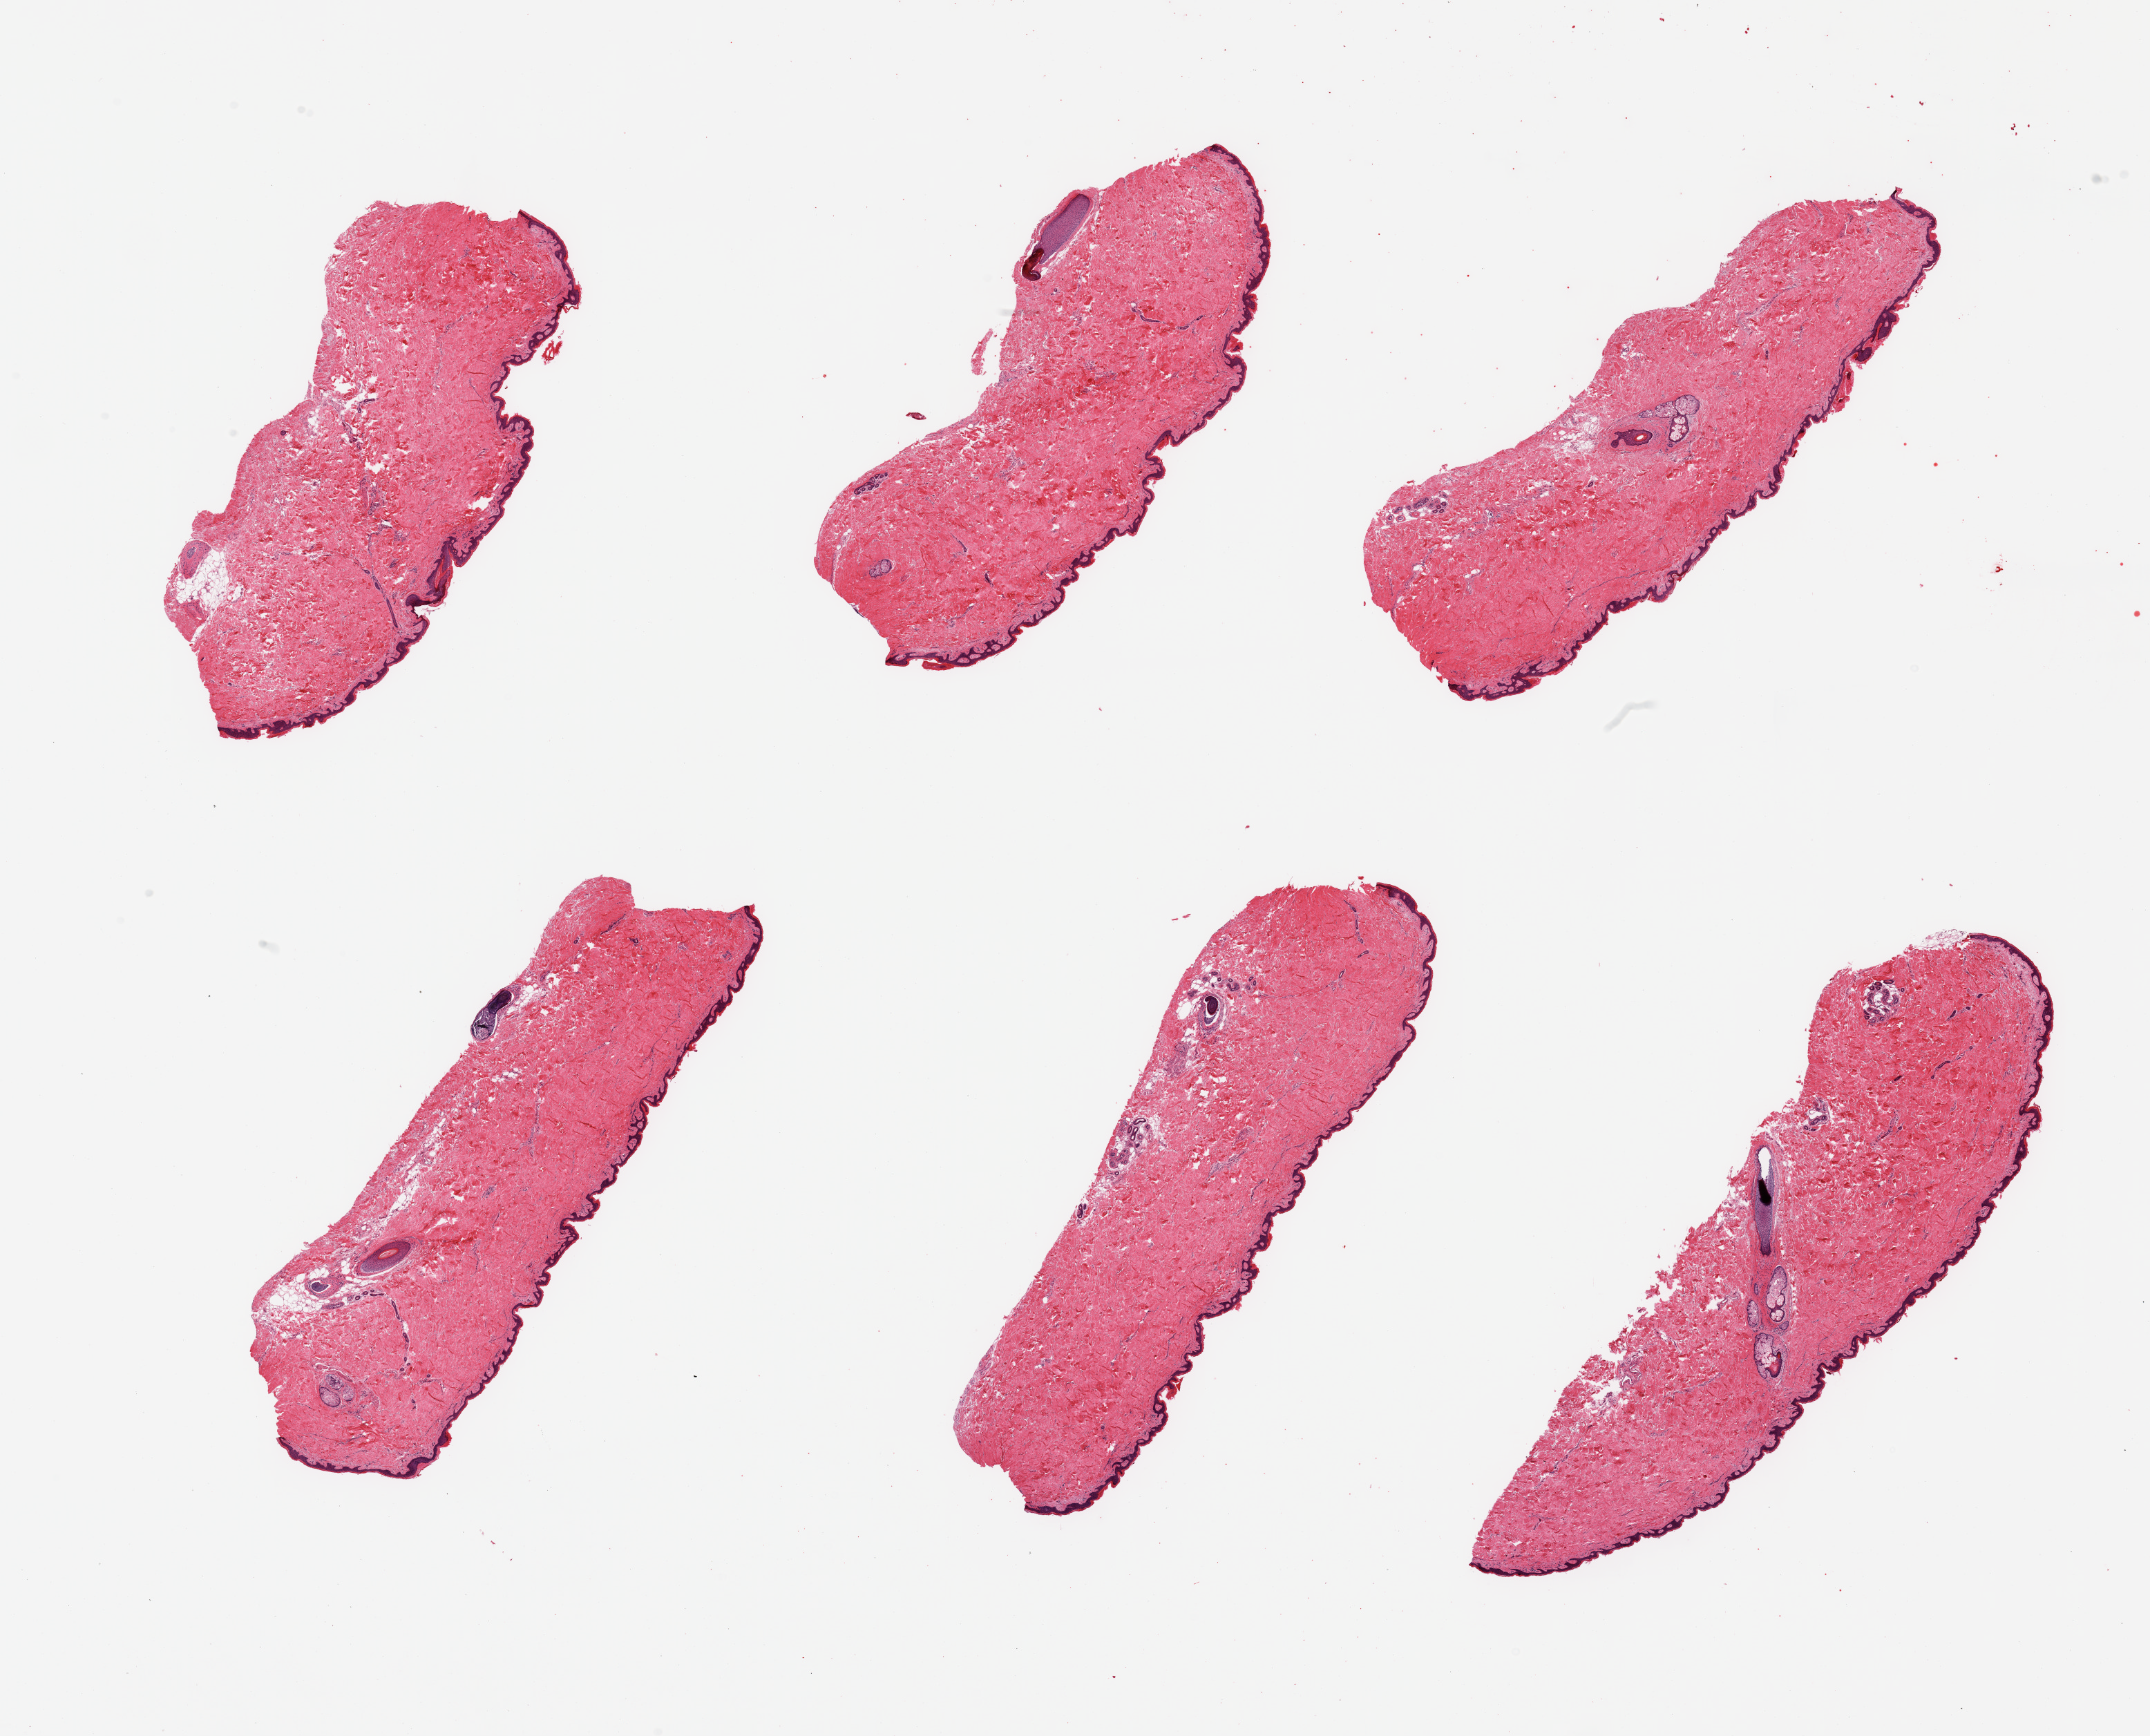
Whole-slide image, haematoxylin and eosin stain — shown as a low-resolution overview of the whole scanned area (about 24.6 x 19.9 mm), PAXgene-fixed paraffin-embedded (PFPE) section, target tissue: skin of suprapubic region, tissue donor sample. Donor sex: male.
• pathologist's review note for this sample: 6 pieces, no significant dermal fat/ squamous epithelium is ~20-40 microns